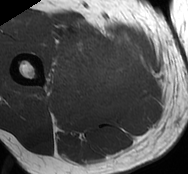
MRI of an extremity soft-tissue mass, one axial slice; position 27 of 93 along the scan axis; MR volume resampled by the dataset authors to the PET/CT grid (not the native acquisition matrix); 3.27 mm slice thickness; 188 × 174 image matrix, field of view 184 × 170 mm. Male patient. From the clinical record (not read from this slice): histological type: undifferentiated - pleiomorphic; grade: high; site of the primary tumour: right thigh.
Annotated regions visible in this slice (expert contour drawn on MRI and transferred to this co-registered scan by the dataset authors):
- gross tumour volume including surrounding oedema: bounding box (x1, y1, x2, y2) in pixels: (47, 26, 137, 91)
- gross tumour volume (mass): (84, 37, 137, 82)